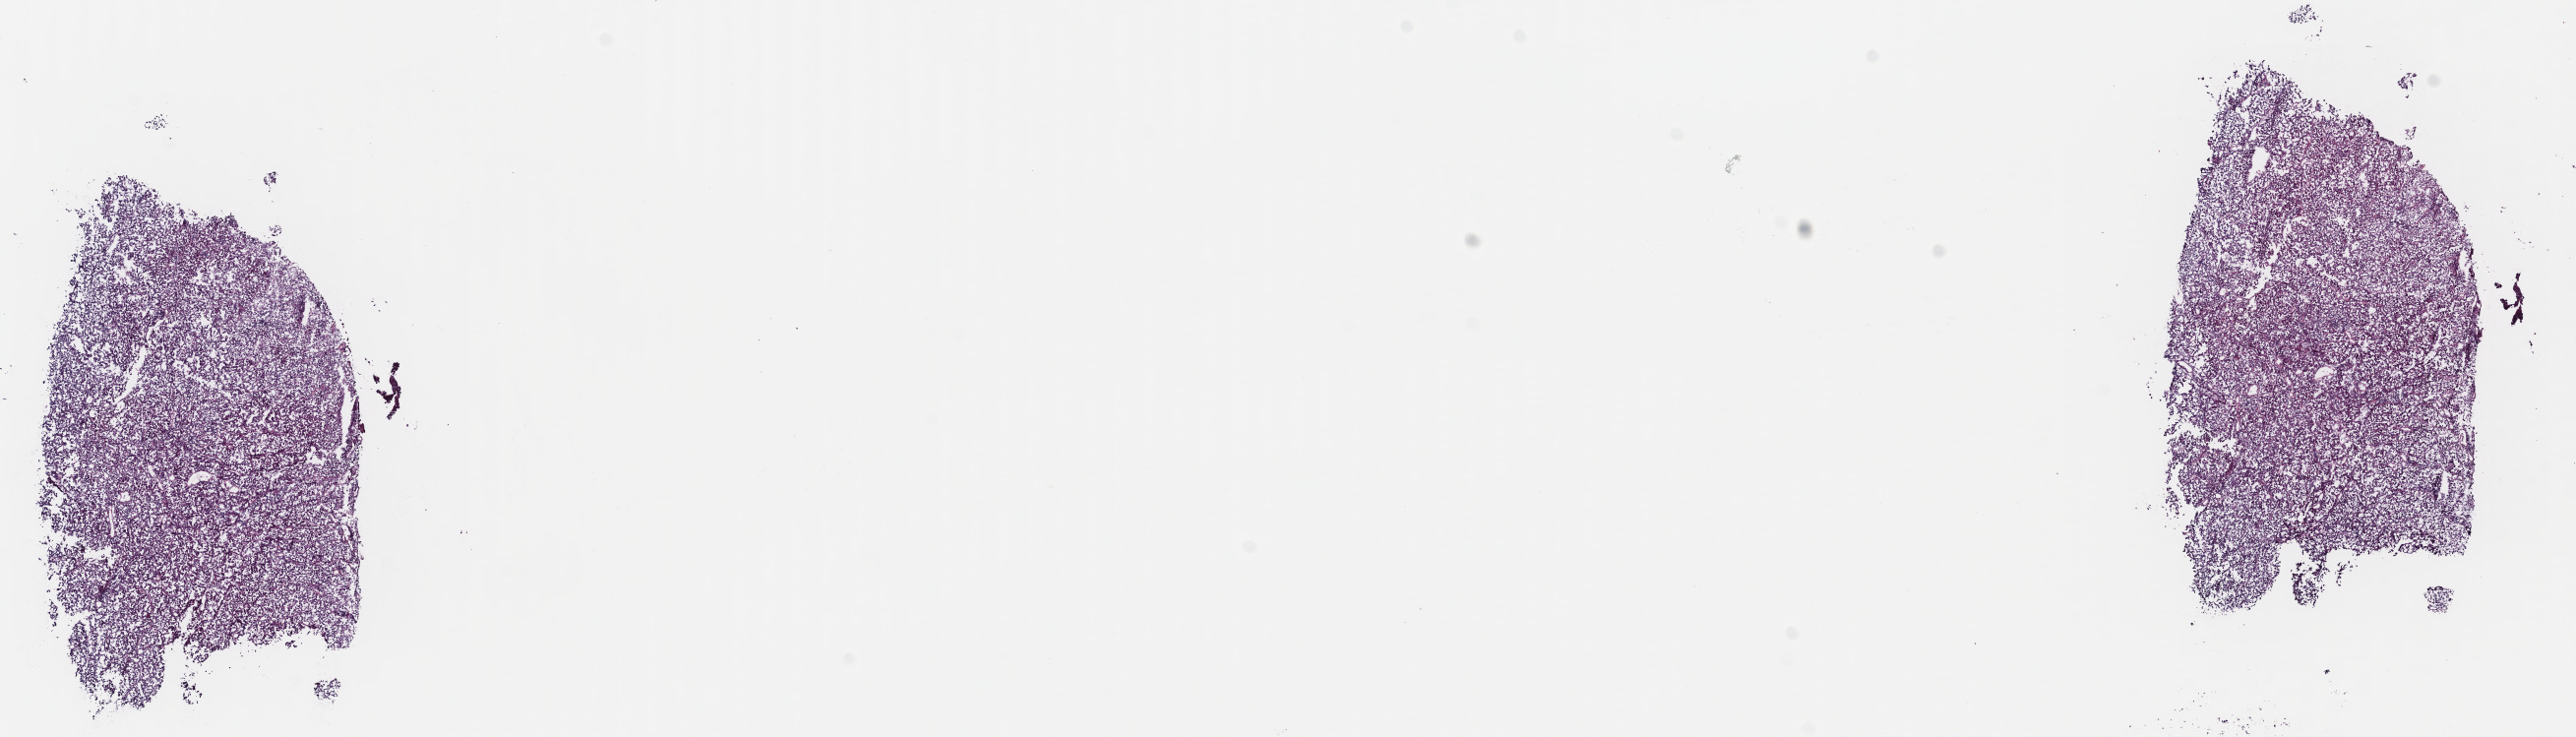
Whole-slide histology image, H&E — whole scanned area (about 20.6 x 5.9 mm, from a 40x scan) shown as a low-resolution overview, frozen section from the top of the tissue portion, primary tumour sample from the bladder. Patient: male, age at initial diagnosis 57 years. Histologic grade: high grade. Pathologist review of this section (percent, as recorded): tumour cells 85%, tumour nuclei 85%, normal cells 0%, stromal cells 15%, necrosis 0%. Infiltration values recorded for this section: lymphocyte infiltration 0%, monocyte infiltration 0%, neutrophil infiltration 0%.
AJCC pathologic stage: II. Diagnosis: Transitional cell carcinoma (posterior wall of bladder).